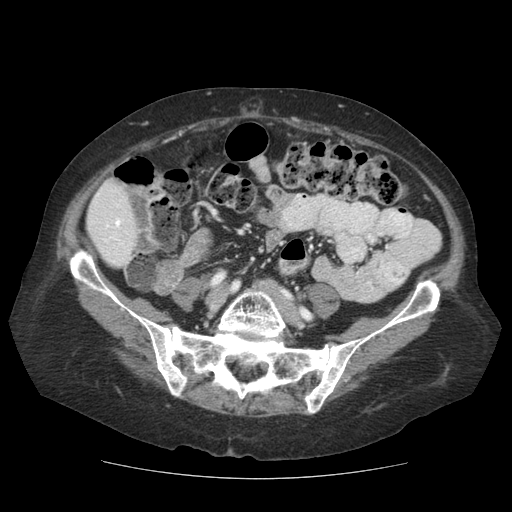
Contrast-enhanced abdominal CT (liver protocol), one axial slice. Soft-tissue window (W 400 / L 40 HU). 512 × 512 image matrix, field of view 360 × 360 mm. Case-level facts recorded for this patient, not image findings: diagnosis: hepatocellular carcinoma (patient treated with transarterial chemoembolisation; whether this scan precedes or follows treatment is not stated here); TNM stage (as recorded): Stage-I; Child-Pugh class: A; tumour differentiation: moderately-poorly differentiated; tumour nodularity: uninodular.
Annotated regions visible in this slice (semi-automatically segmented with operator editing):
- liver parenchyma outside the tumour (the mass and vessels are separate outlines, so this box may not span the whole liver): bounding box [x1, y1, x2, y2] px = [86, 180, 138, 266]
- liver vessels: [115, 218, 121, 227]